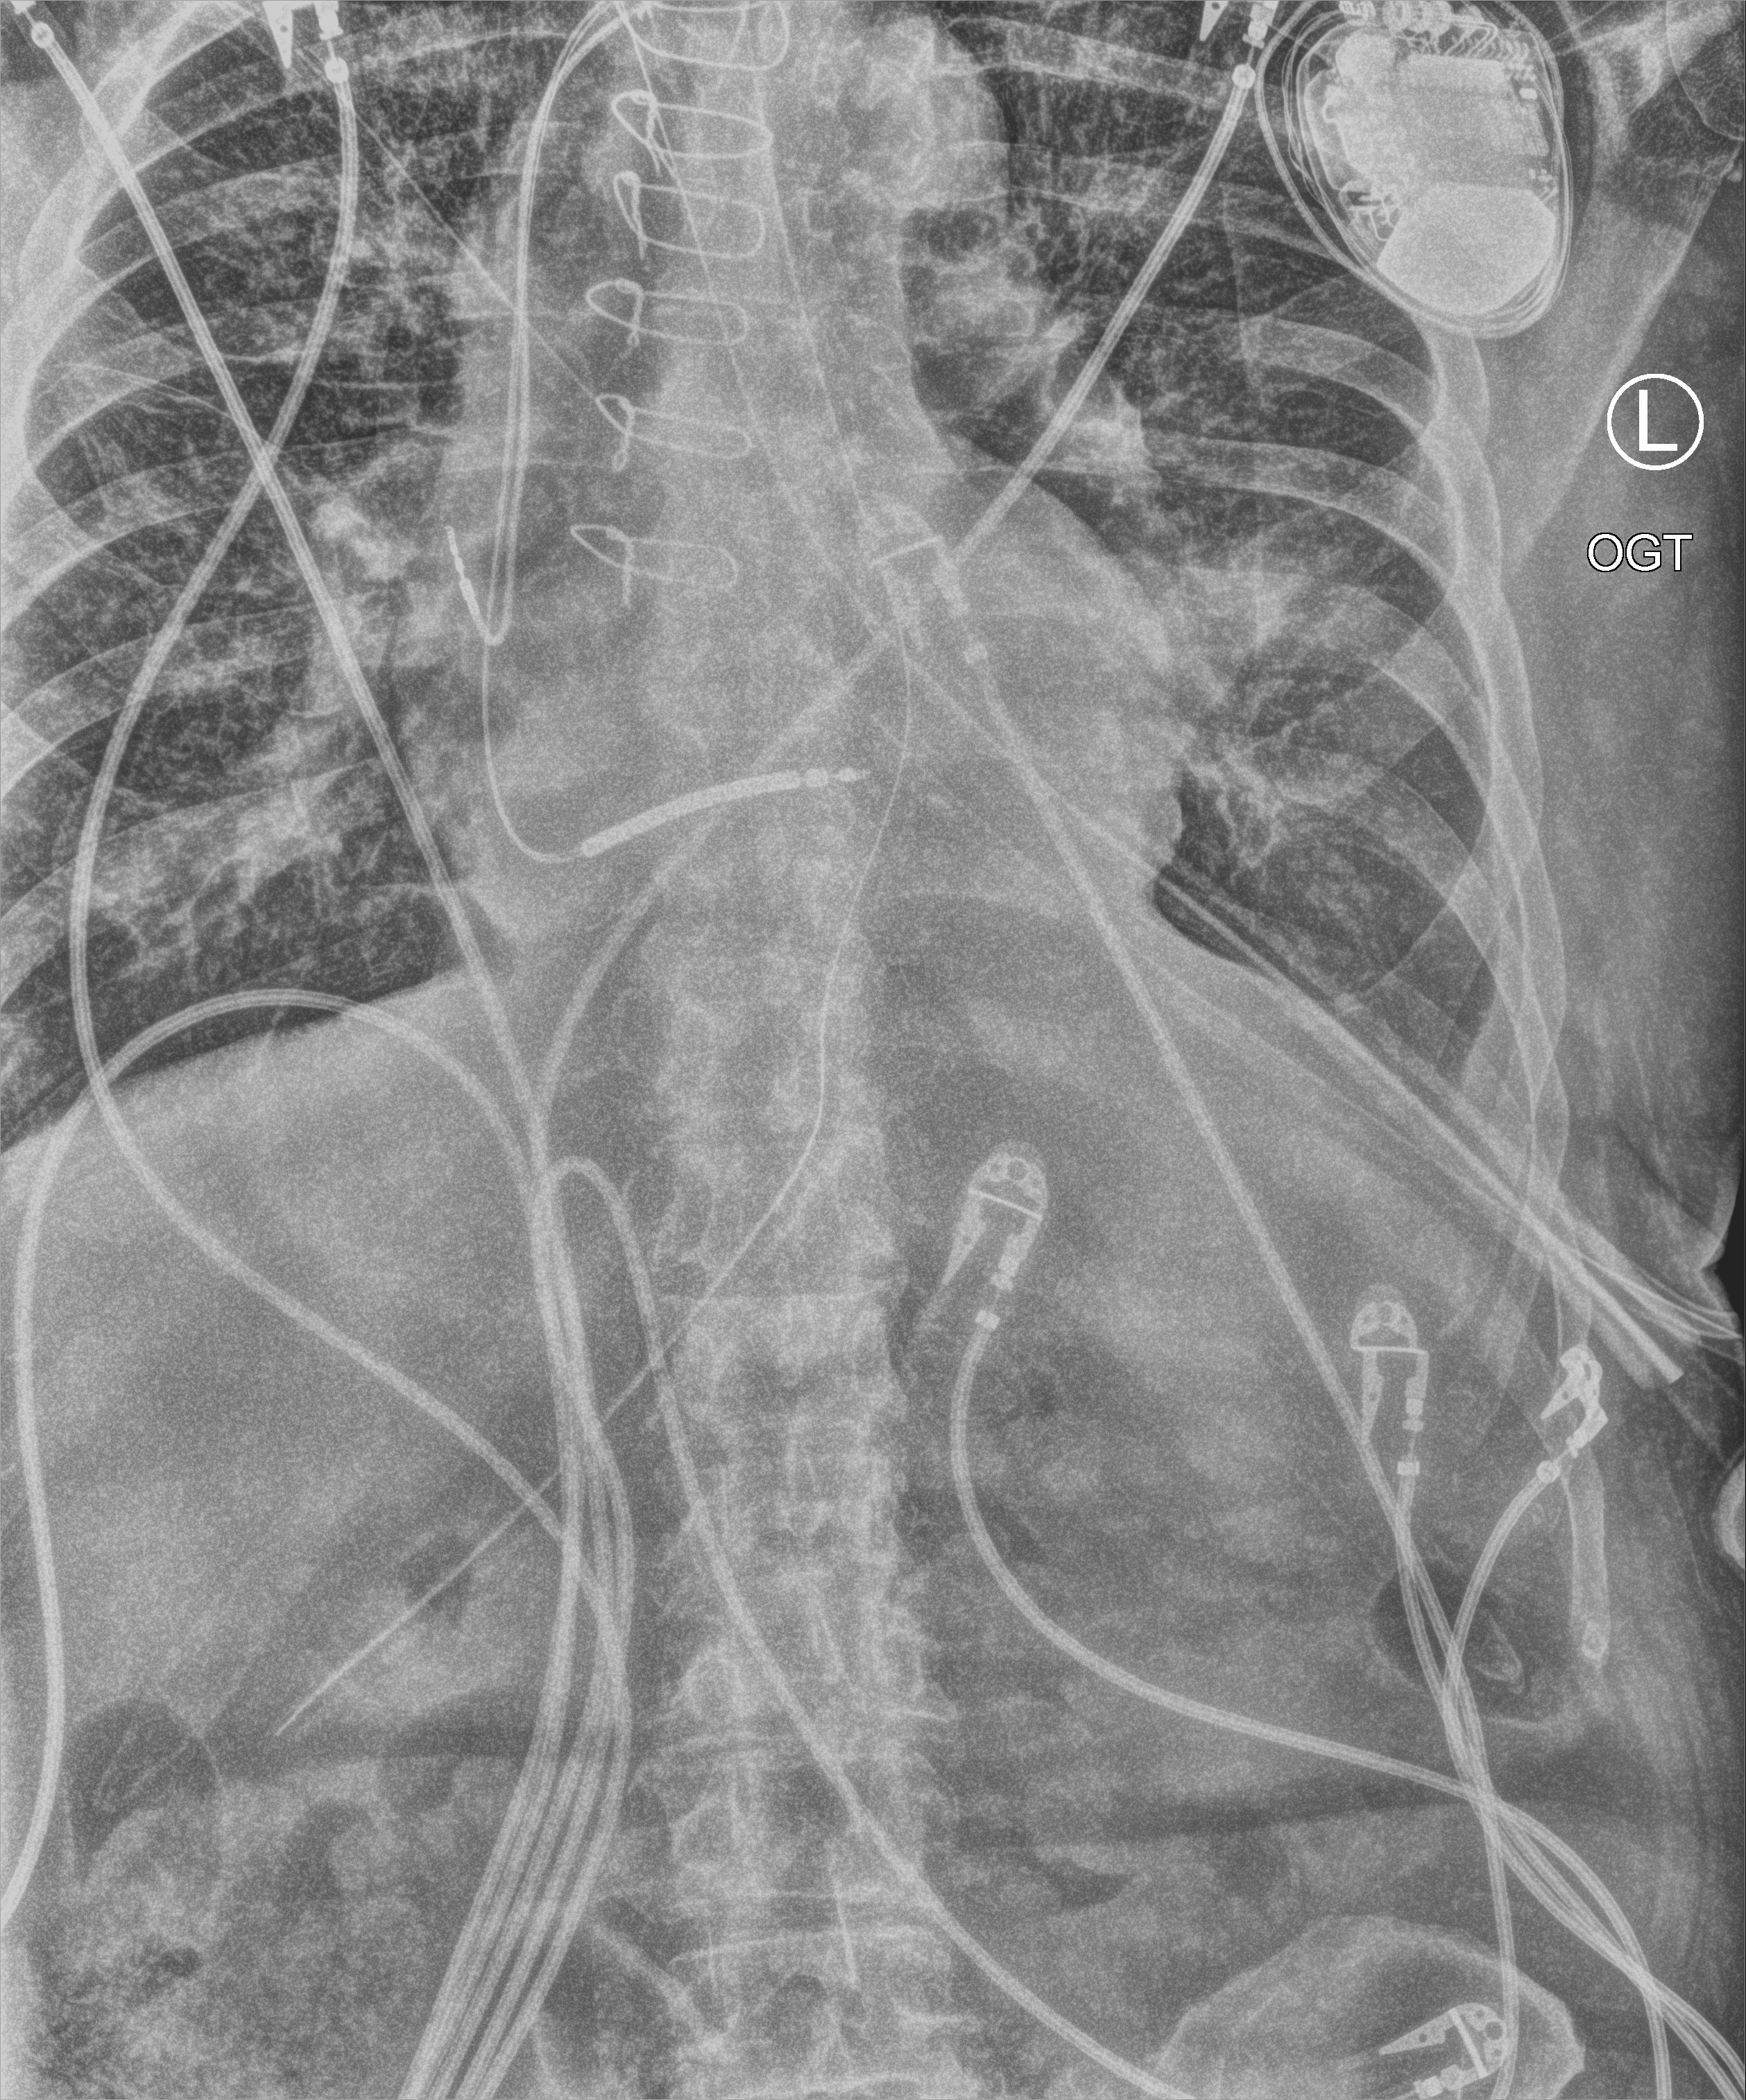
Portable chest radiograph; anteroposterior (AP) projection. Patient hospitalised with COVID-19; male, aged 75–90 years.
From the hospital-stay record, not from the radiograph (when in the stay this image was taken is not recorded): admitted to intensive care during this hospital stay: yes.